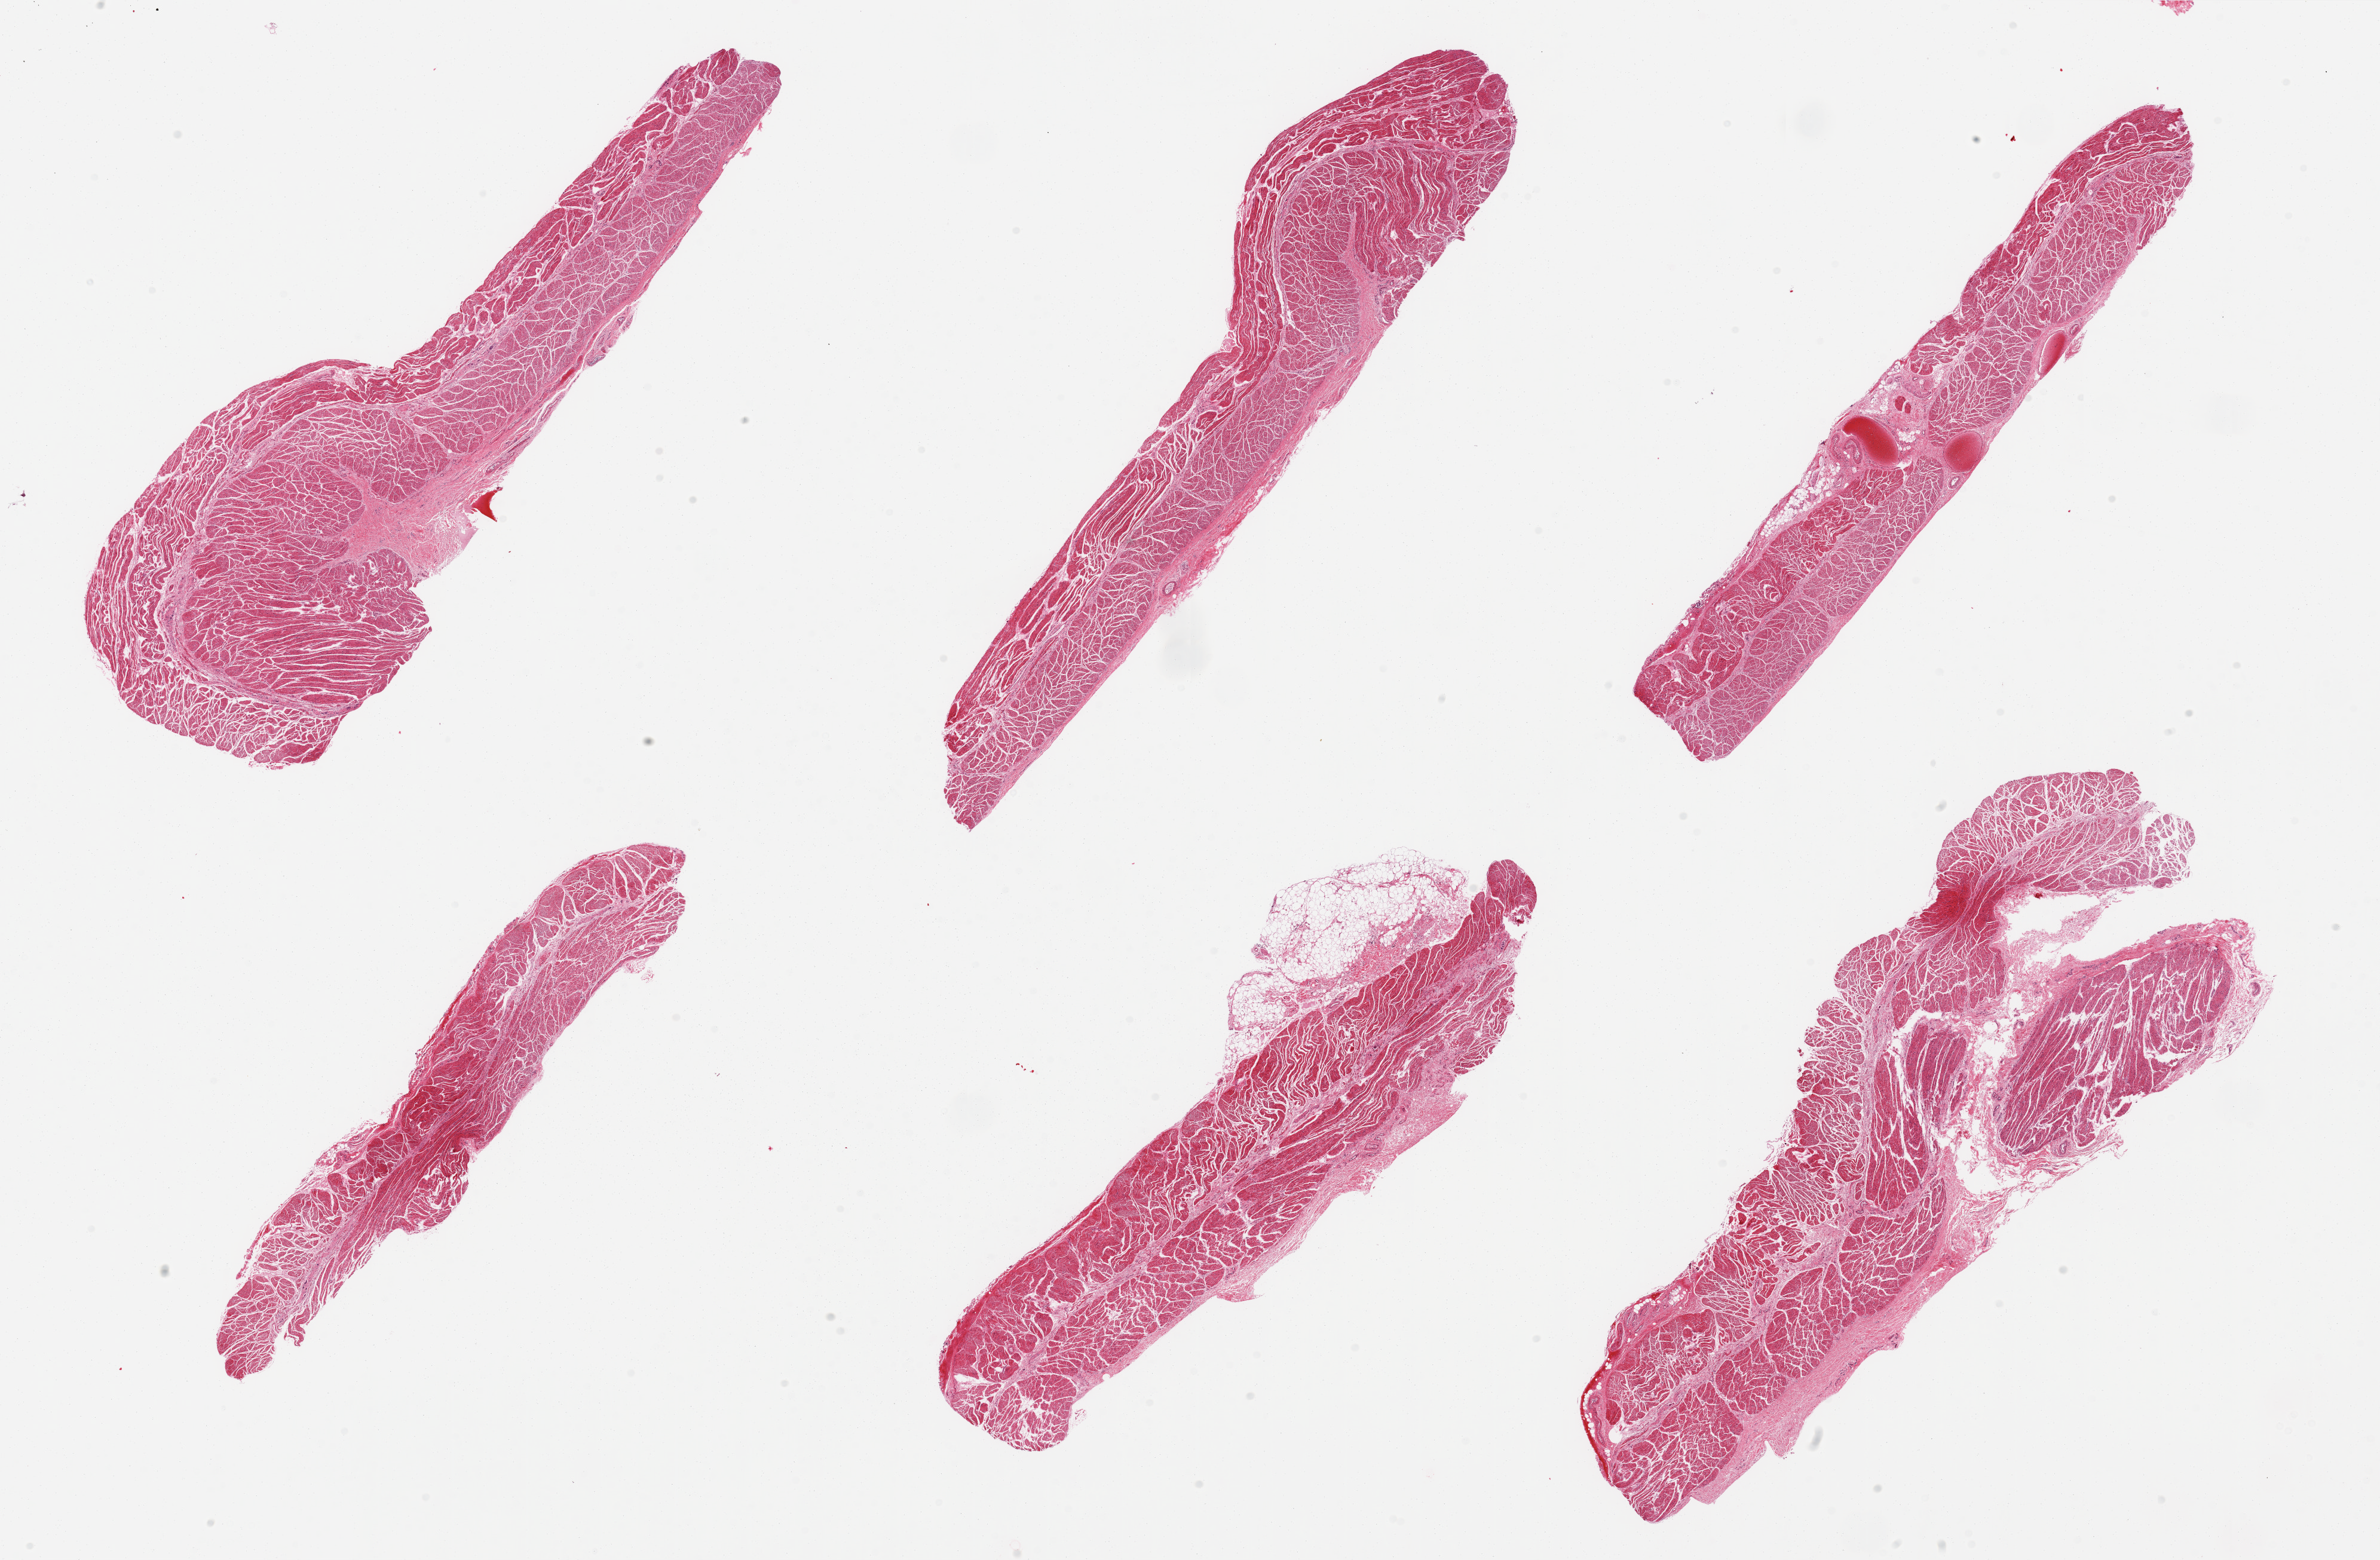
Digitized hematoxylin and eosin (H&E)-stained section — low-resolution overview of the scanned area, about 31.5 x 20.7 mm (acquisition: 20x scan), PAXgene-fixed, paraffin-embedded tissue, sampled site (target tissue): esophageal muscle, tissue donor sample. Donor sex: male.
- review note (as recorded): 6 pieces; well dissected muscularis